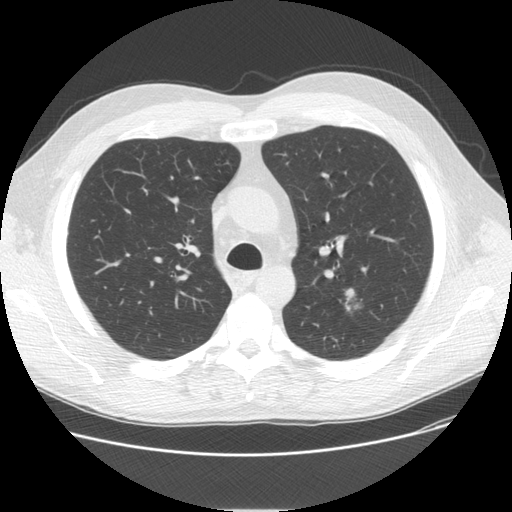
Low-dose screening chest CT, one axial slice; position 109 of 150 along the scan axis; reconstruction kernel STANDARD; 120 kVp; lung window (W 1500 / L -600 HU); 512 × 512 image matrix, field of view 370 × 370 mm.
Structures marked on this image (expert manual segmentation):
- lesion 1 (tumor, upper lobe of left lung): box from (x=345, y=289) to (x=364, y=311) px